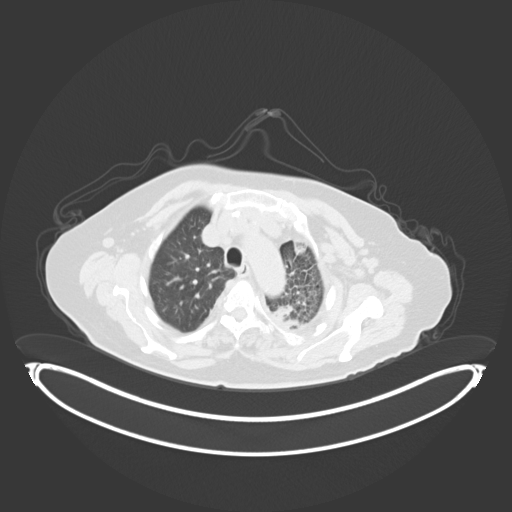
Chest CT, one axial slice; position 223 of 284 along the scan axis; lung window (W 1500 / L -600 HU); 3 mm slice thickness; 512 × 512 image matrix. Patient: female, 75 years. Case-level facts recorded for this patient, not image findings: clinical TNM (as recorded): T3 N3 M1.
Outlined on this slice (rectangle marked by the reading radiologist):
- lung tumour (recorded histology: adenocarcinoma): bounding box <269,296,302,329> (left, top, right, bottom; pixels)